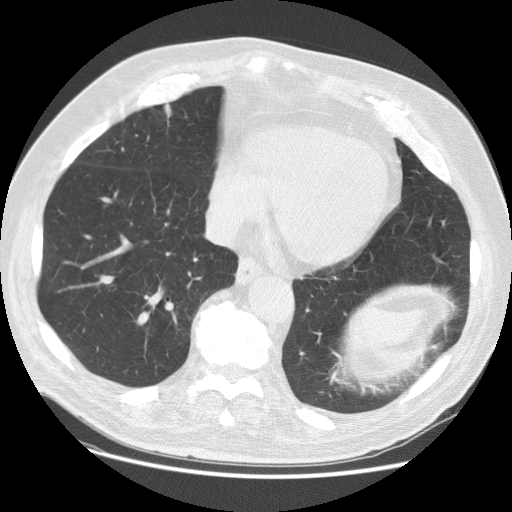
Low-dose screening chest CT, one axial slice. Reconstruction kernel STANDARD. 140 kVp. Lung window (W 1500 / L -600 HU). 2.5 mm slice thickness. 512 × 512 image matrix.
Annotated regions visible in this slice (manually delineated by an expert):
- lesion 1 (tumor, upper lobe of right lung): bounding box [x1, y1, x2, y2] px = [164, 103, 172, 115]